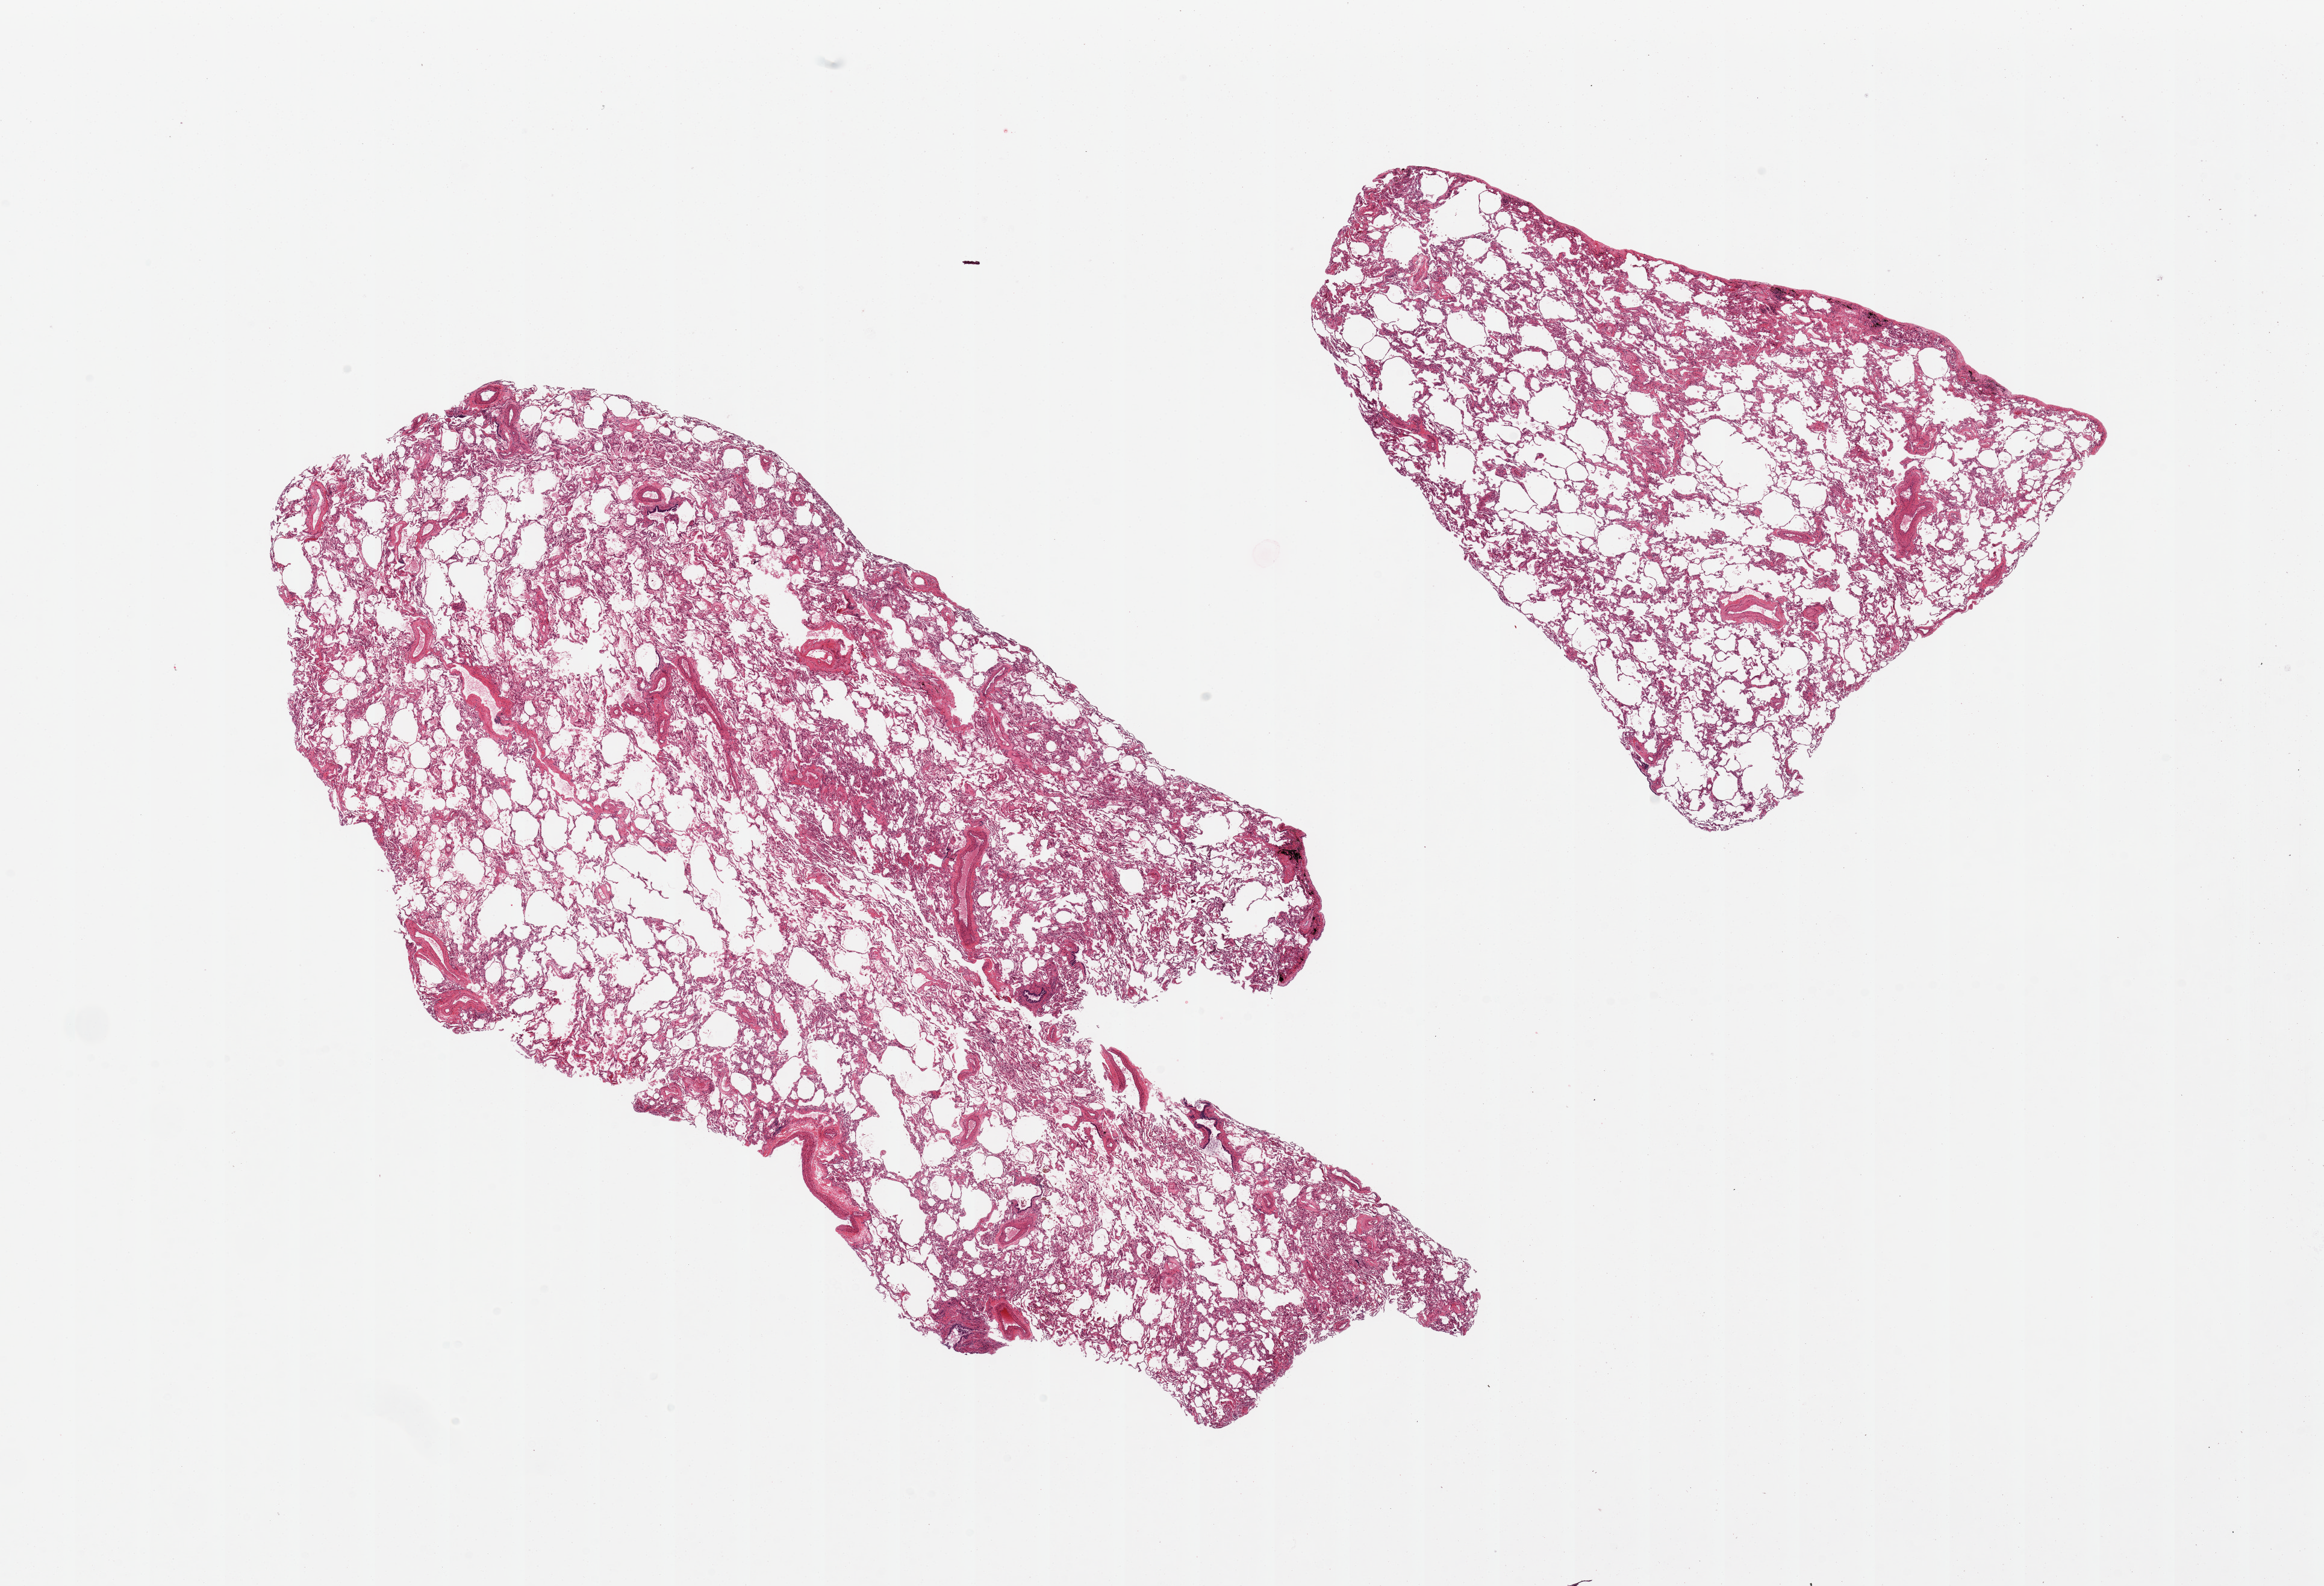
Digitized haematoxylin and eosin-stained section, a low-resolution overview of the entire scanned area, about 30.5 x 20.8 mm (from a 20x scan), PAXgene-fixed, paraffin-embedded tissue, sampled site (target tissue): lung, tissue donor sample. Donor: female.
Reviewer comment on this tissue sample: 2 pieces, some emphysematous change, hemosiderin-laden macrophages.